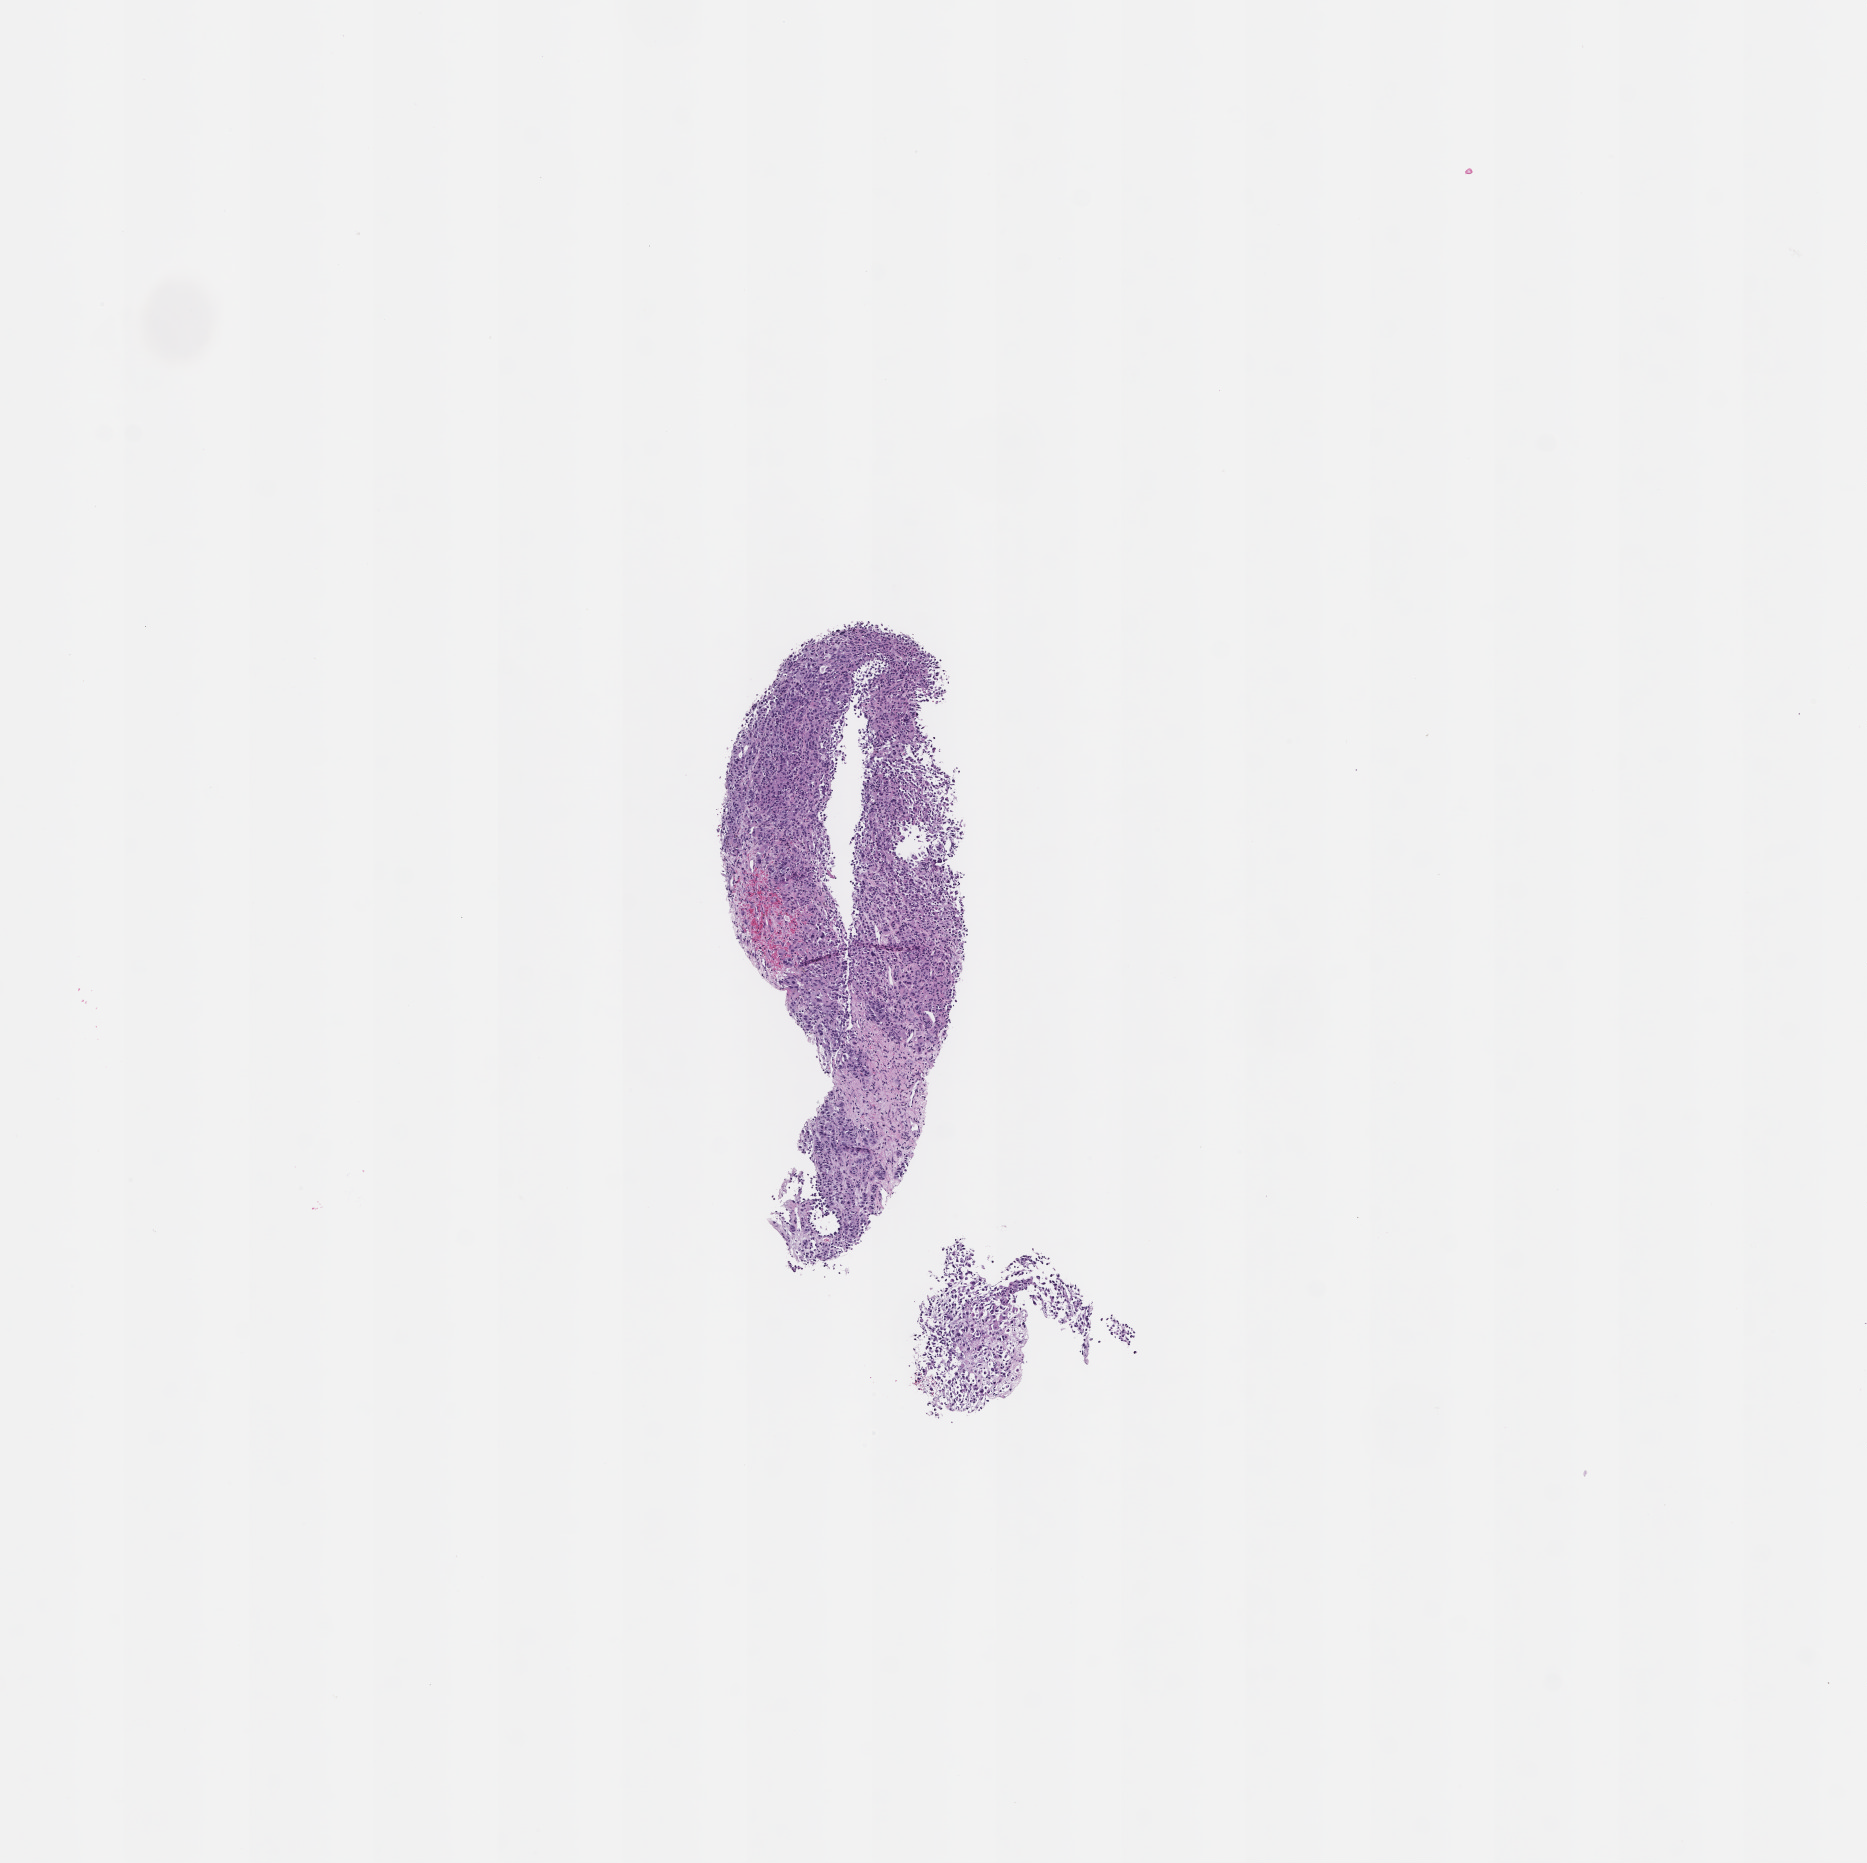
Digitized haematoxylin and eosin-stained section, a low-resolution overview of the entire scanned area, about 7.5 x 7.5 mm; formalin-fixed paraffin-embedded section; collected at baseline (before treatment). Patient sex: male.
This section: metastasis (sampled organ not recorded). Patient diagnosis (primary): Melanoma.